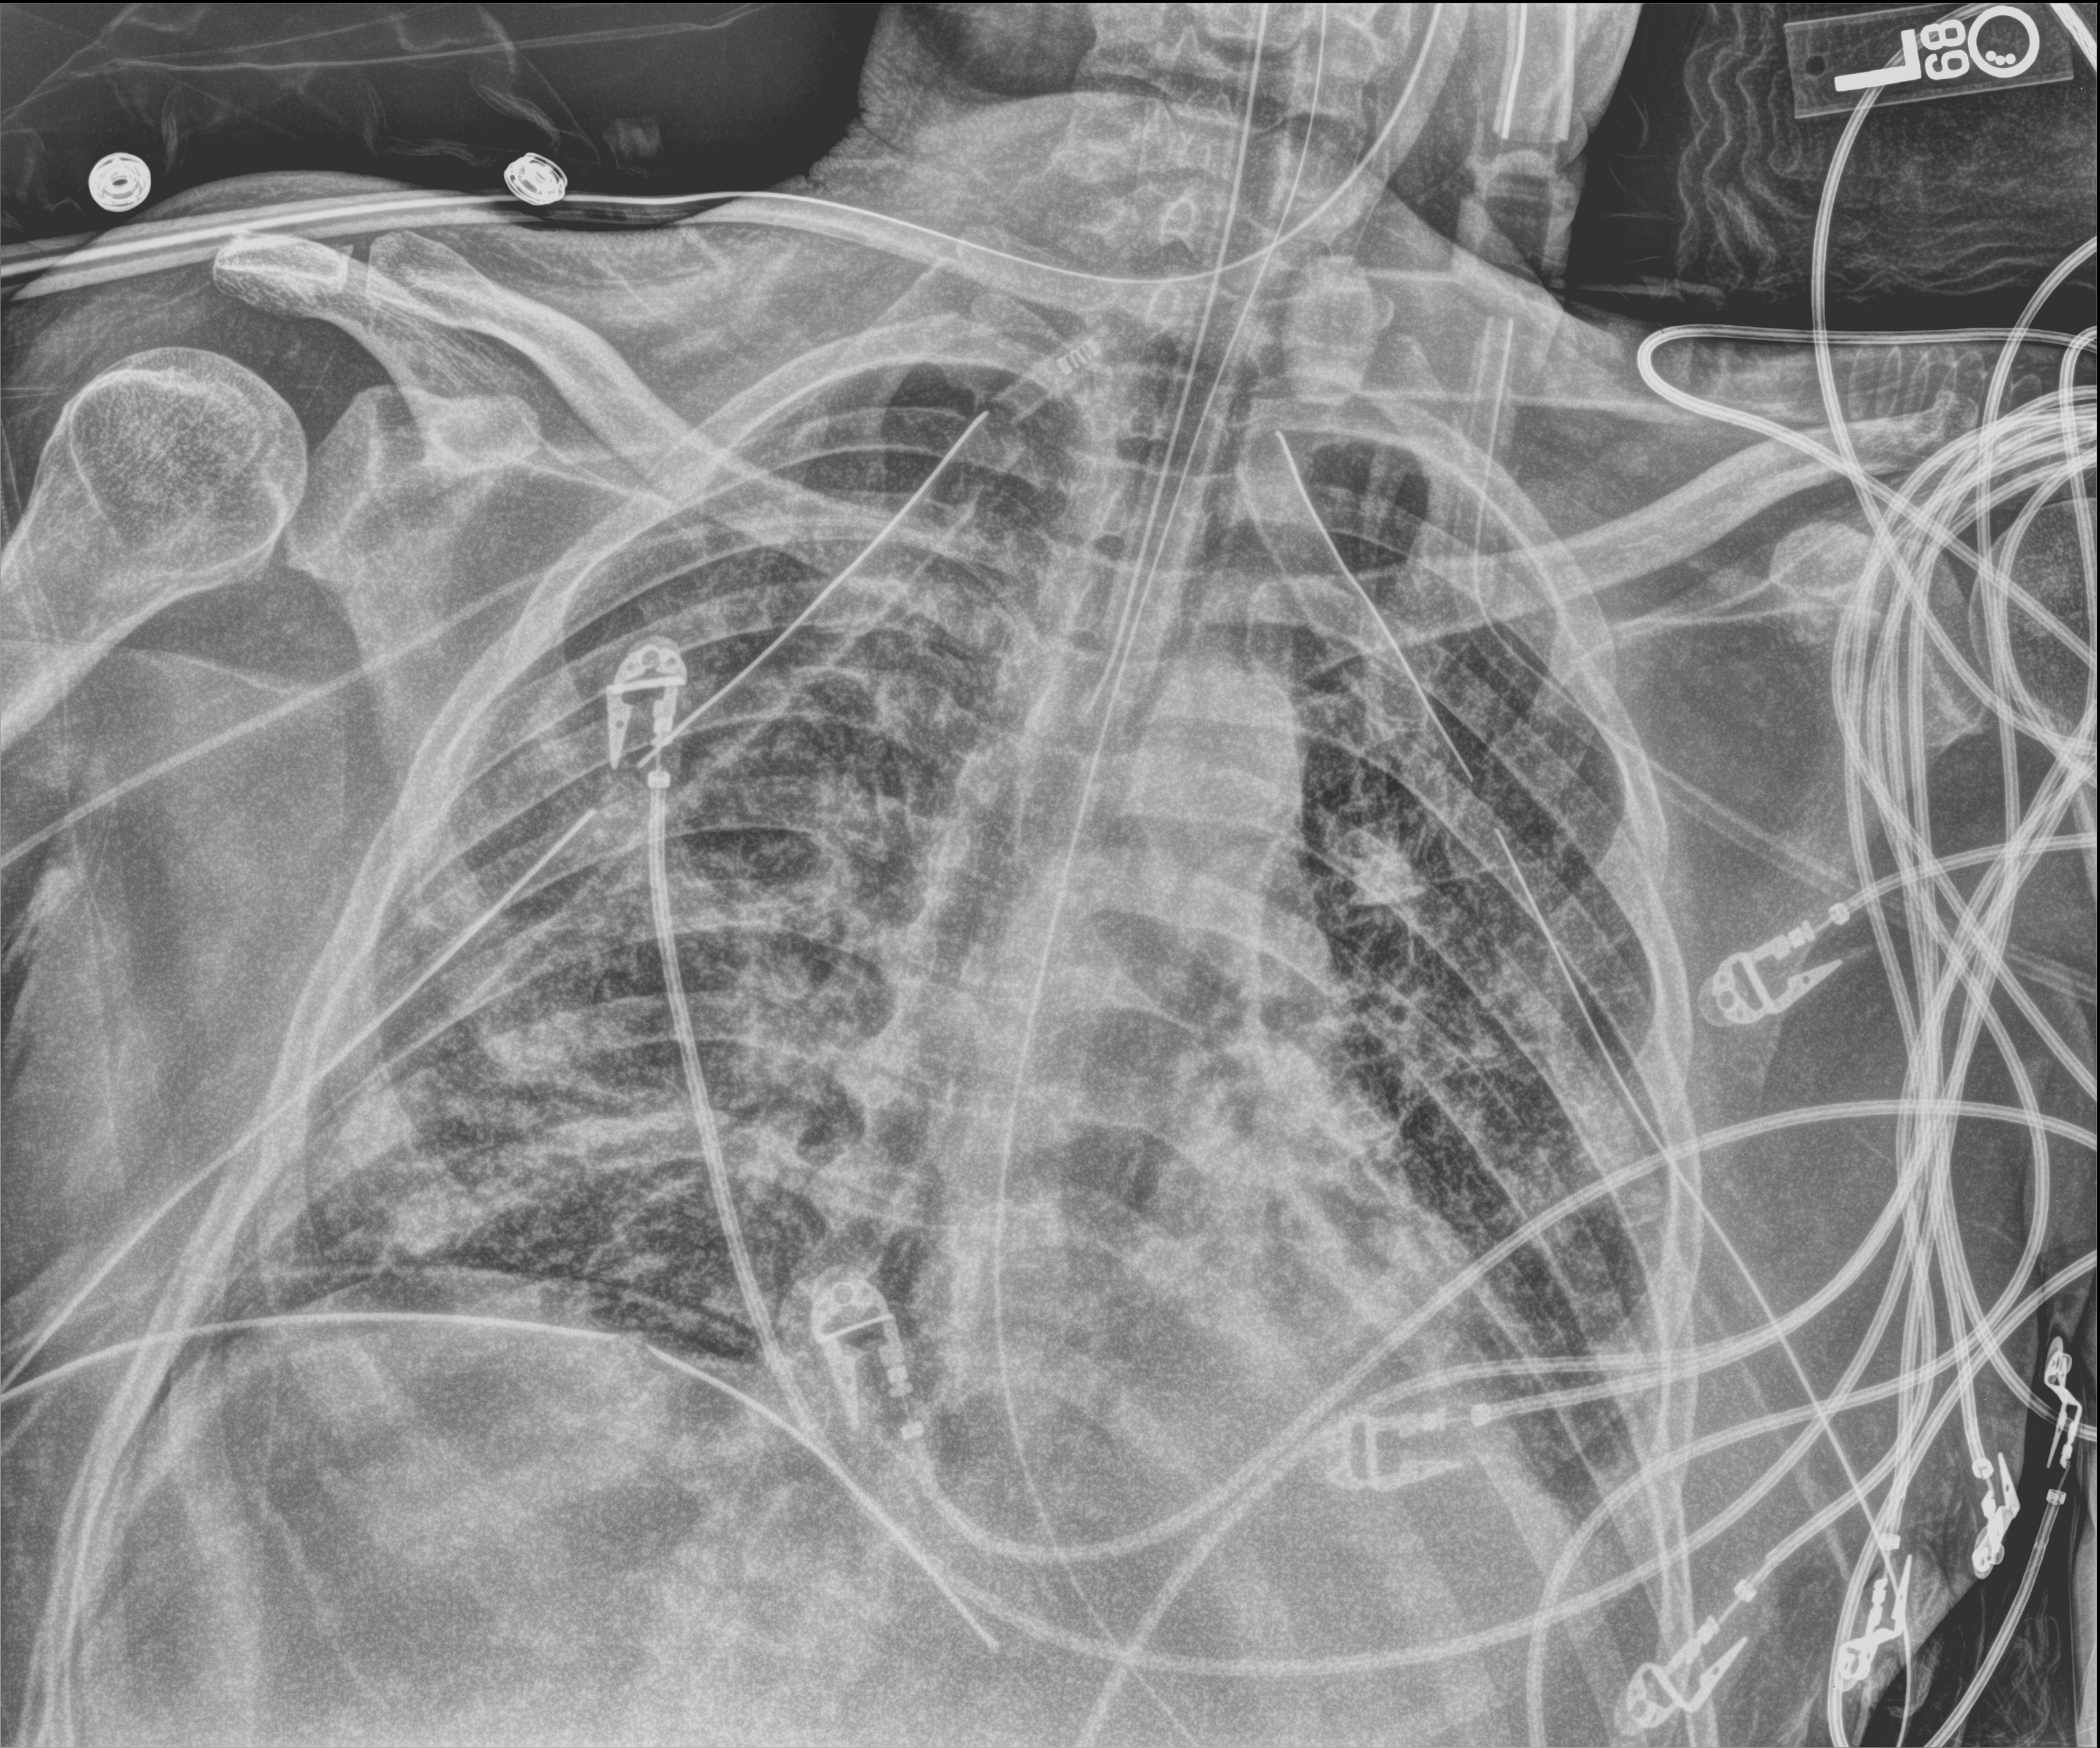
Portable chest radiograph, anteroposterior (AP) projection. Male patient hospitalised with COVID-19, age 18–59 years.
From the hospital-stay record, not from the radiograph (when in the stay this image was taken is not recorded):
- mechanically ventilated during this hospital stay: yes
- admitted to intensive care during this hospital stay: yes